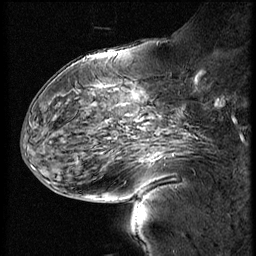
Breast MRI (dynamic contrast-enhanced), one sagittal slice; position 24 of 60 along the scan axis; 4 images stored at this slice position (order not interpretable as contrast timing); 1.5 T; TE 4.2 ms, TR 9 ms; 2.5 mm slice thickness; 256 × 256 image matrix, field of view 180 × 180 mm. Female patient, age 56 years. From the clinical record (not read from this slice): setting: breast cancer imaged before/during neoadjuvant chemotherapy; receptor status: HER2-positive.
Outlined on this slice (semi-automatically segmented with operator editing):
- analysis volume of interest (the breast-tissue region the enhancement analysis was run in; not a lesion): bounding box <110,138,192,201> (left, top, right, bottom; pixels)
- tumour enhancement mask (voxels above the 140 % enhancement threshold inside the analysis volume of interest): <152,160,155,162>